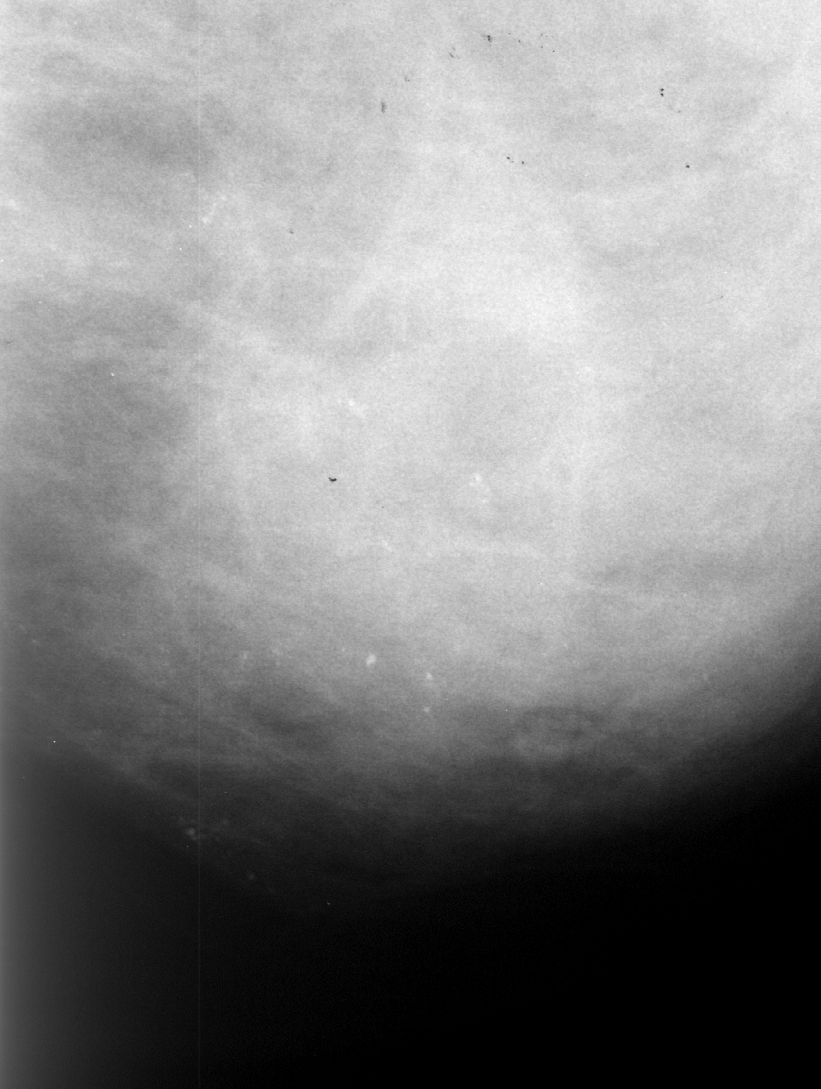
Region of interest cut from a scanned film mammogram (one marked finding); left breast; MLO view; BI-RADS breast density category 4 (scale 1–4).
Marked abnormality: calcifications, morphology pleomorphic, distribution segmental; BI-RADS assessment category 4; pathology result (as recorded, not read from the image): benign.